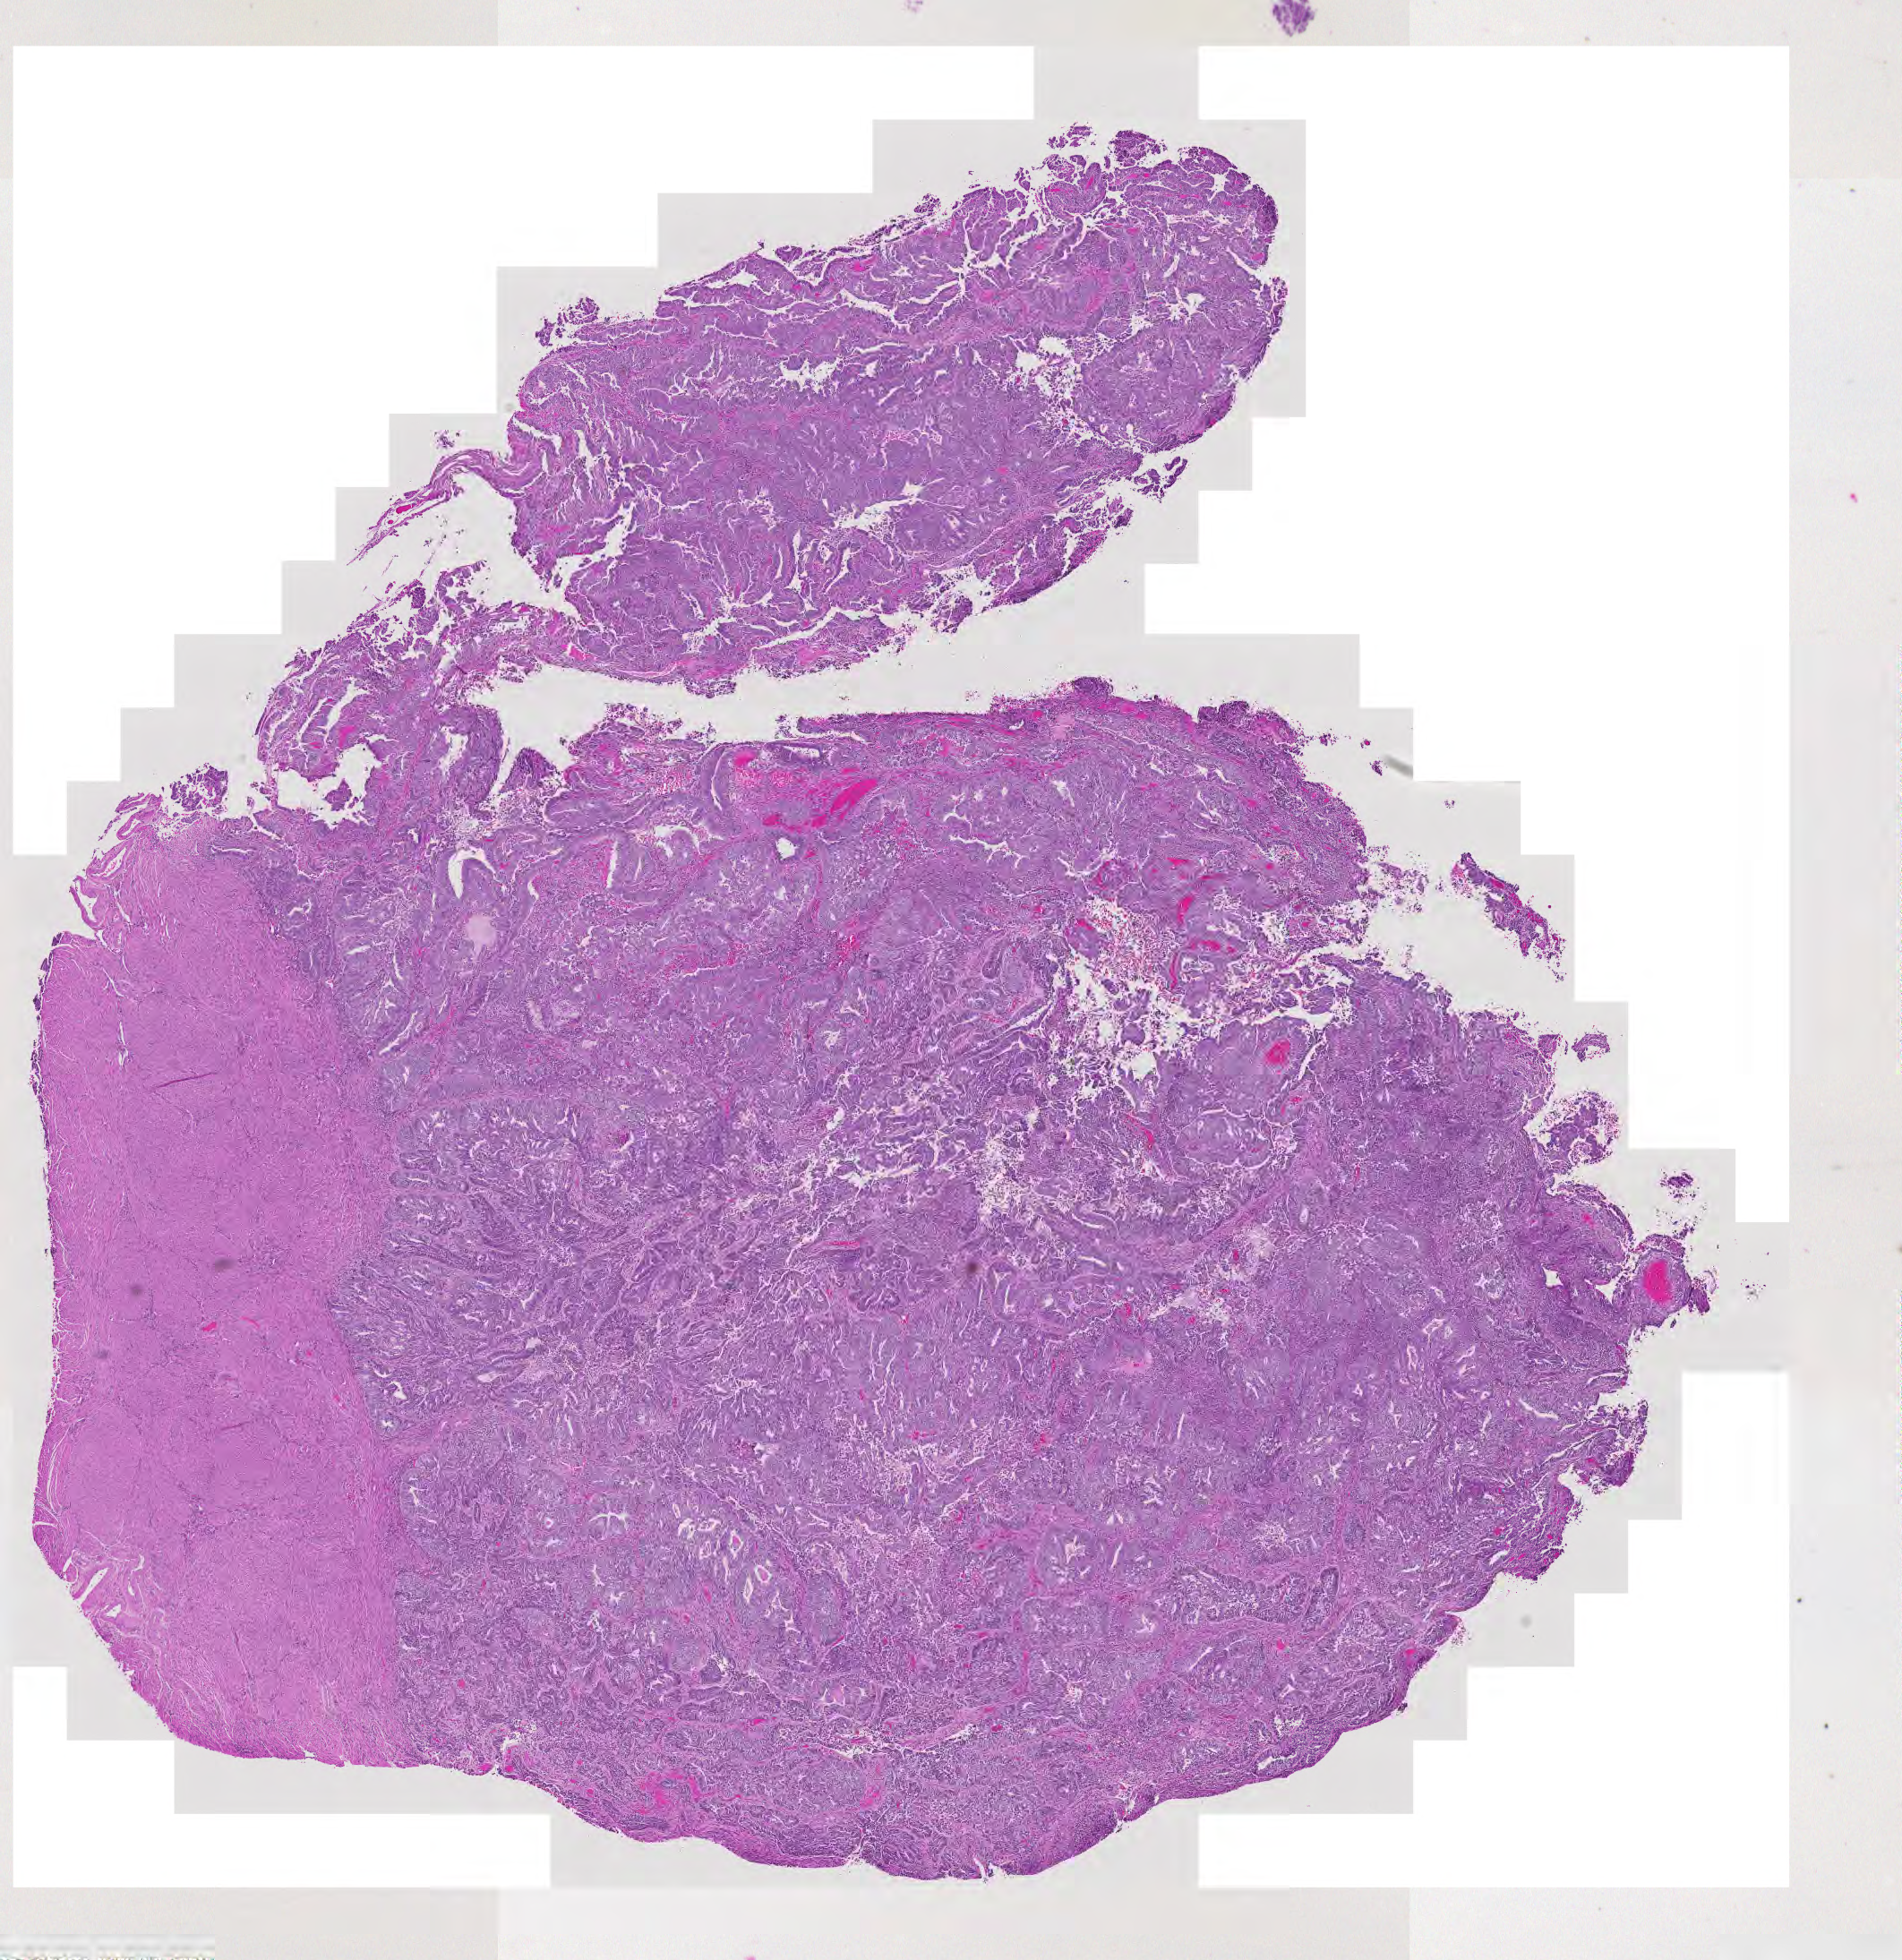
Whole-slide histology image, H&E-stained — a low-resolution overview of the entire scanned area, about 11.0 x 11.3 mm (slide scanned at 20x), tumour tissue sample, sampled site: uterus. Patient: female, age 54 years.
Diagnosis: Endometrioid adenocarcinoma, NOS.